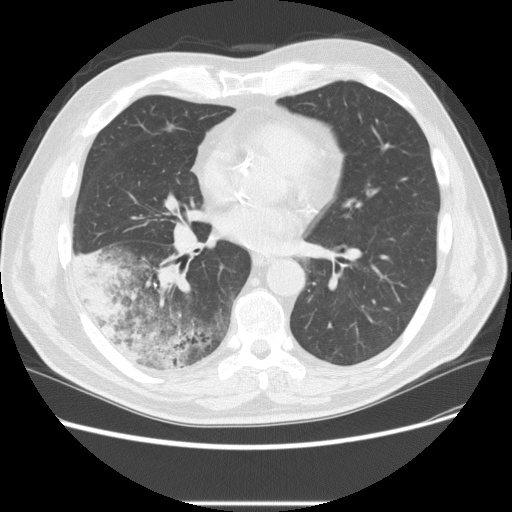
Low-dose screening chest CT, one axial slice. Slice 105 of 233 in the series (ordered by position). 120 kVp. Lung window (W 1500 / L -600 HU). 2.5 mm slice thickness. 512 × 512 image matrix, field of view 380 × 380 mm.
Structures marked on this image (manually delineated by an expert):
- lesion 3 (tumor, lower lobe of right lung): bounding box [x1, y1, x2, y2] px = [73, 250, 128, 319]